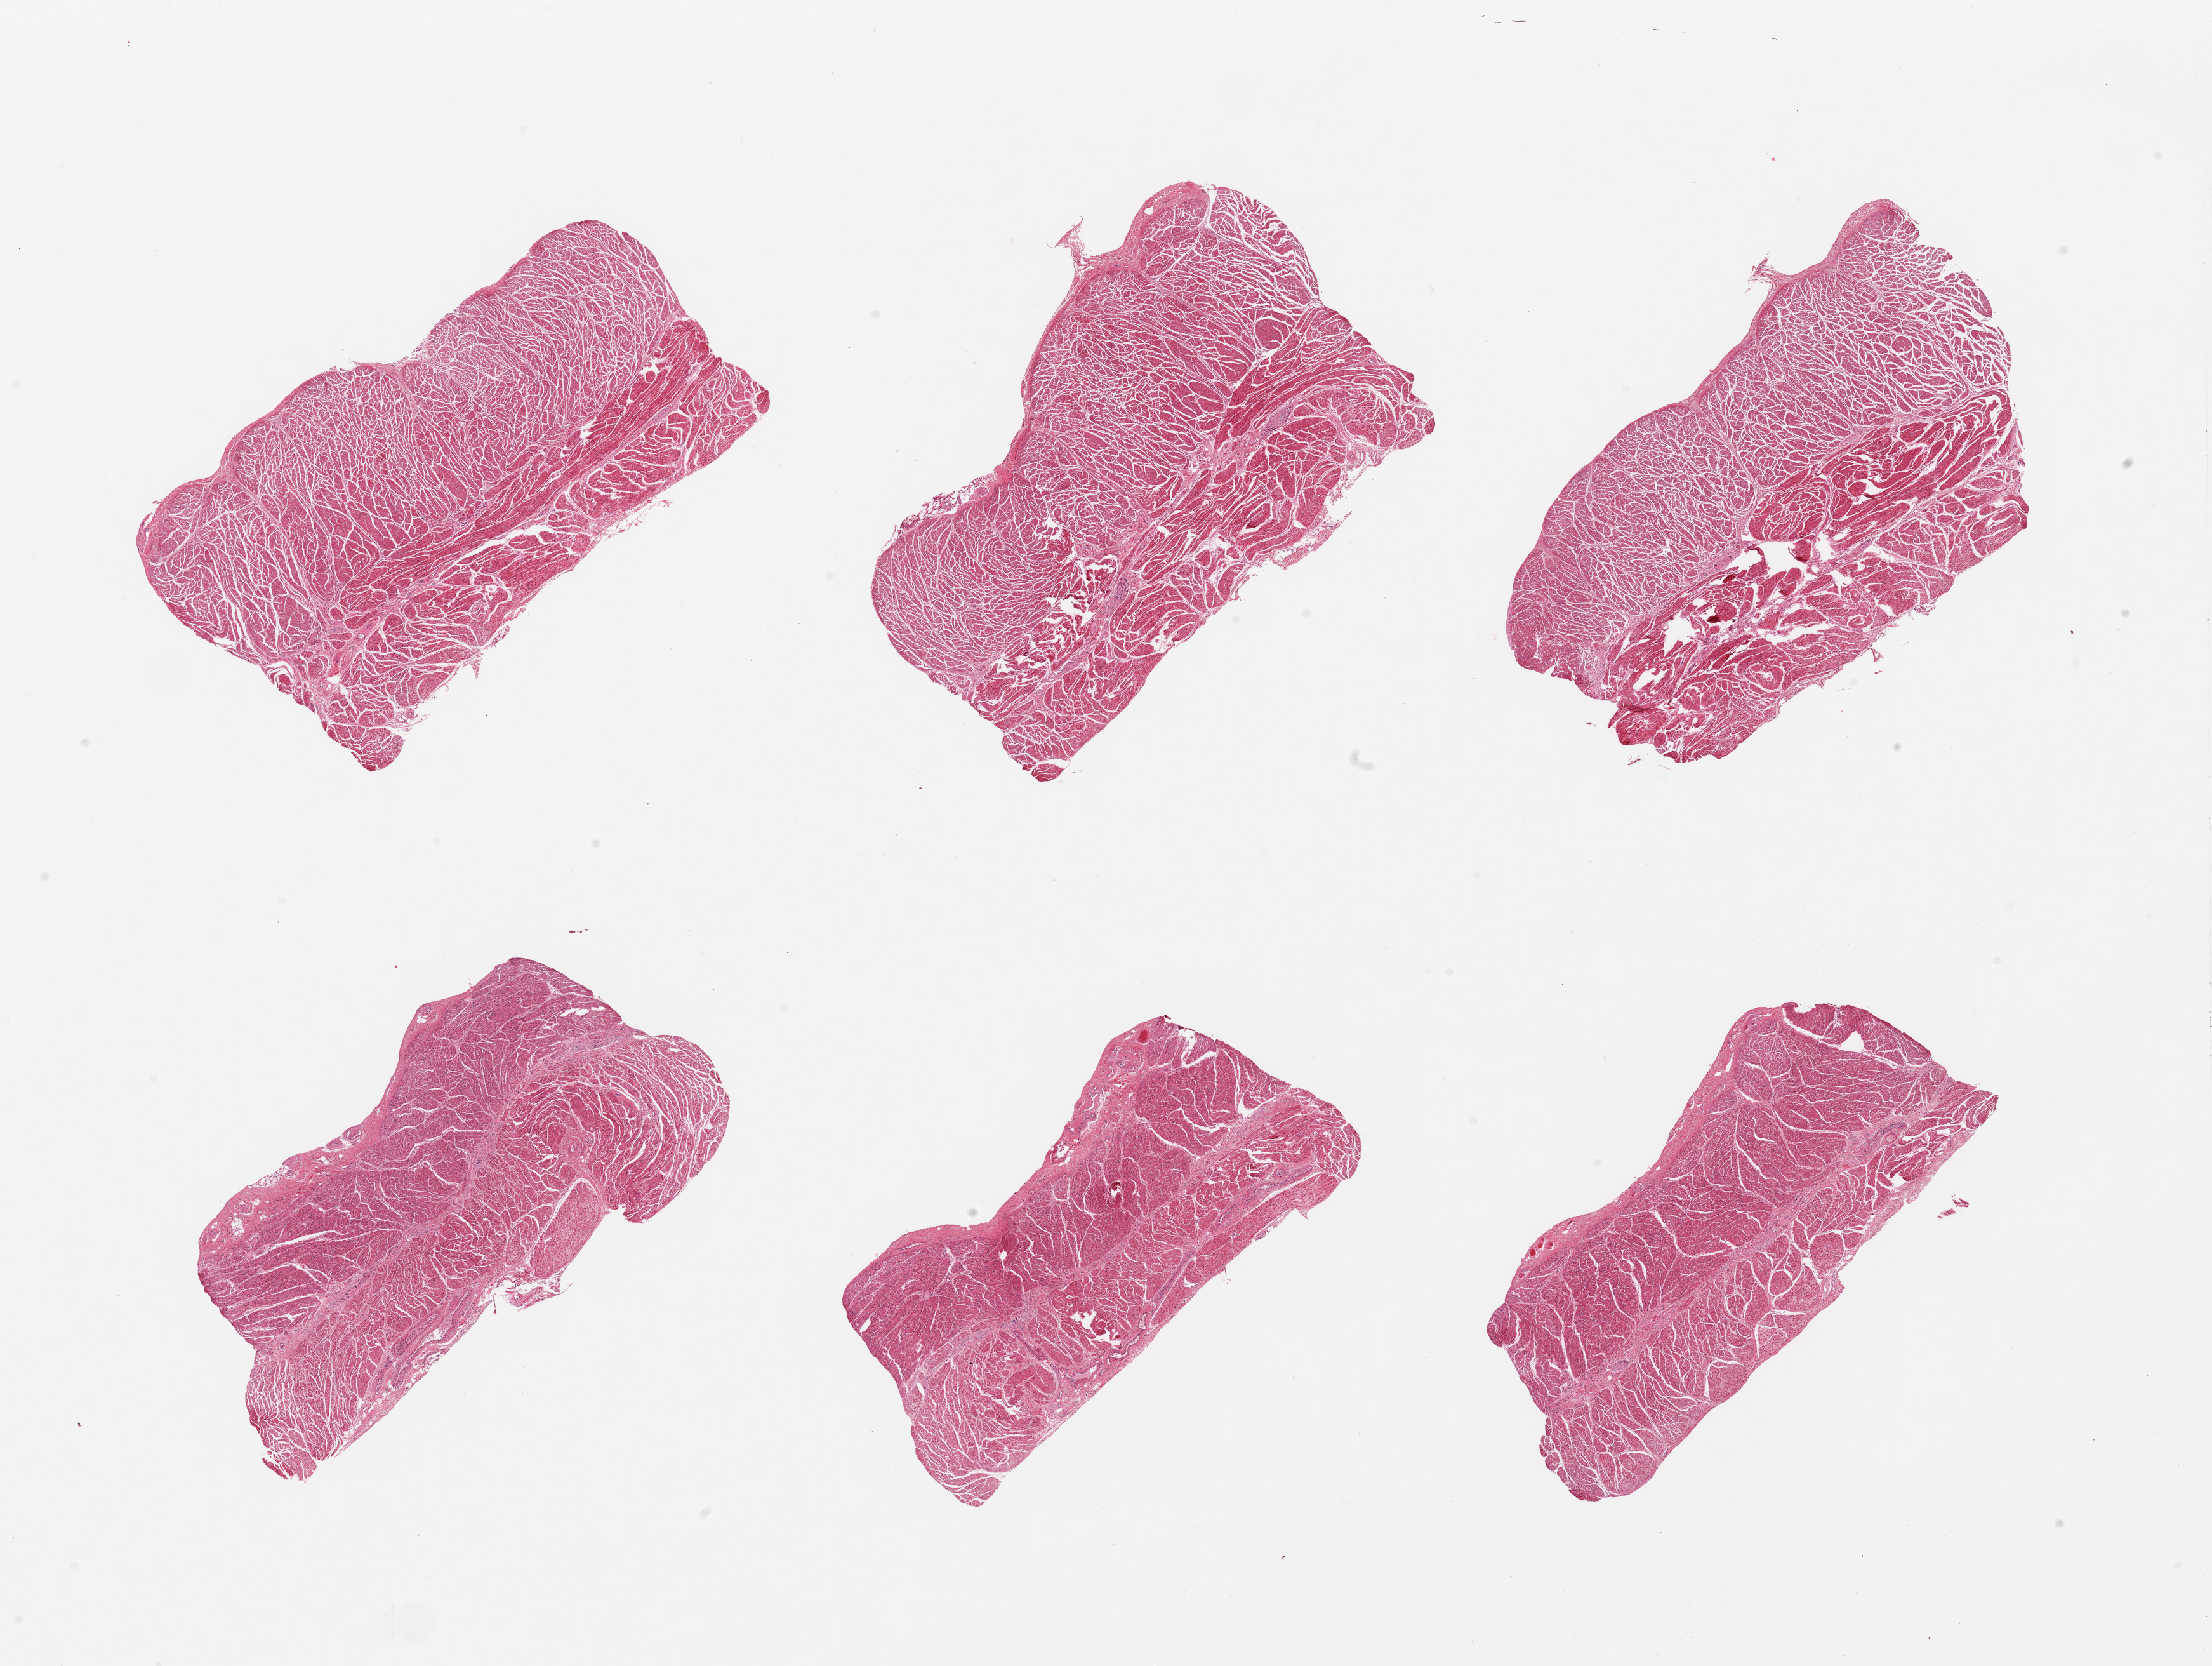
Whole-slide image, hematoxylin and eosin (H&E) stain, whole scanned area (about 27.6 x 20.8 mm, acquisition: 20x scan) shown as a low-resolution overview. PAXgene-fixed, paraffin-embedded tissue. Target tissue: gastroesophageal junction. Donor tissue sample. Male donor.
* review note (as recorded): 6 pieces; well trimmed